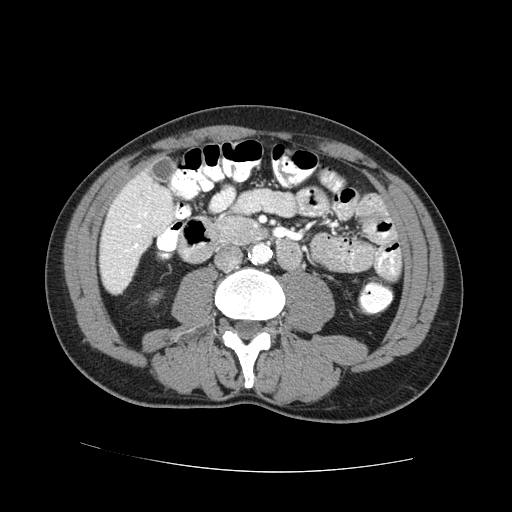
Contrast-enhanced abdominal CT (liver protocol), one axial slice. Position 13 of 73 along the scan axis. 100 kVp. One of 2 acquisitions stored at this slice position. Soft-tissue window (W 400 / L 40 HU). 2.5 mm slice thickness. 512 × 512 image matrix, field of view 380 × 380 mm. From the clinical record (not read from this slice): diagnosis: hepatocellular carcinoma (patient treated with transarterial chemoembolisation; whether this scan precedes or follows treatment is not stated here); TNM stage (as recorded): Stage-IVA; Child-Pugh class: A; tumour nodularity: uninodular.
Structures marked on this image (semi-automatically segmented with operator editing):
- liver parenchyma outside the tumour (the mass and vessels are separate outlines, so this box may not span the whole liver): bounding box [x1, y1, x2, y2] px = [100, 166, 172, 293]
- liver vessels: [125, 213, 147, 252]